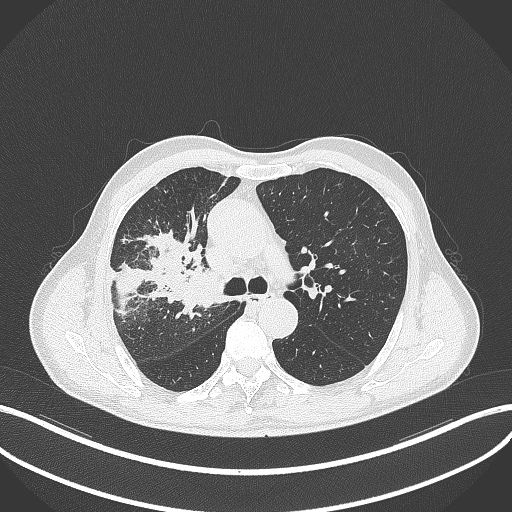
Chest CT, one axial slice; slice 323 of 490 in the series (ordered by position); lung window (W 1500 / L -600 HU); 512 × 512 image matrix, field of view 400 × 400 mm. Male patient, age 69 years. From the clinical record (not read from this slice): clinical TNM (as recorded): T2a N0 M0.
Structures marked on this image (bounding box drawn by a radiologist):
- lung tumour (recorded histology: adenocarcinoma): bounding box <176,264,227,319> (left, top, right, bottom; pixels)